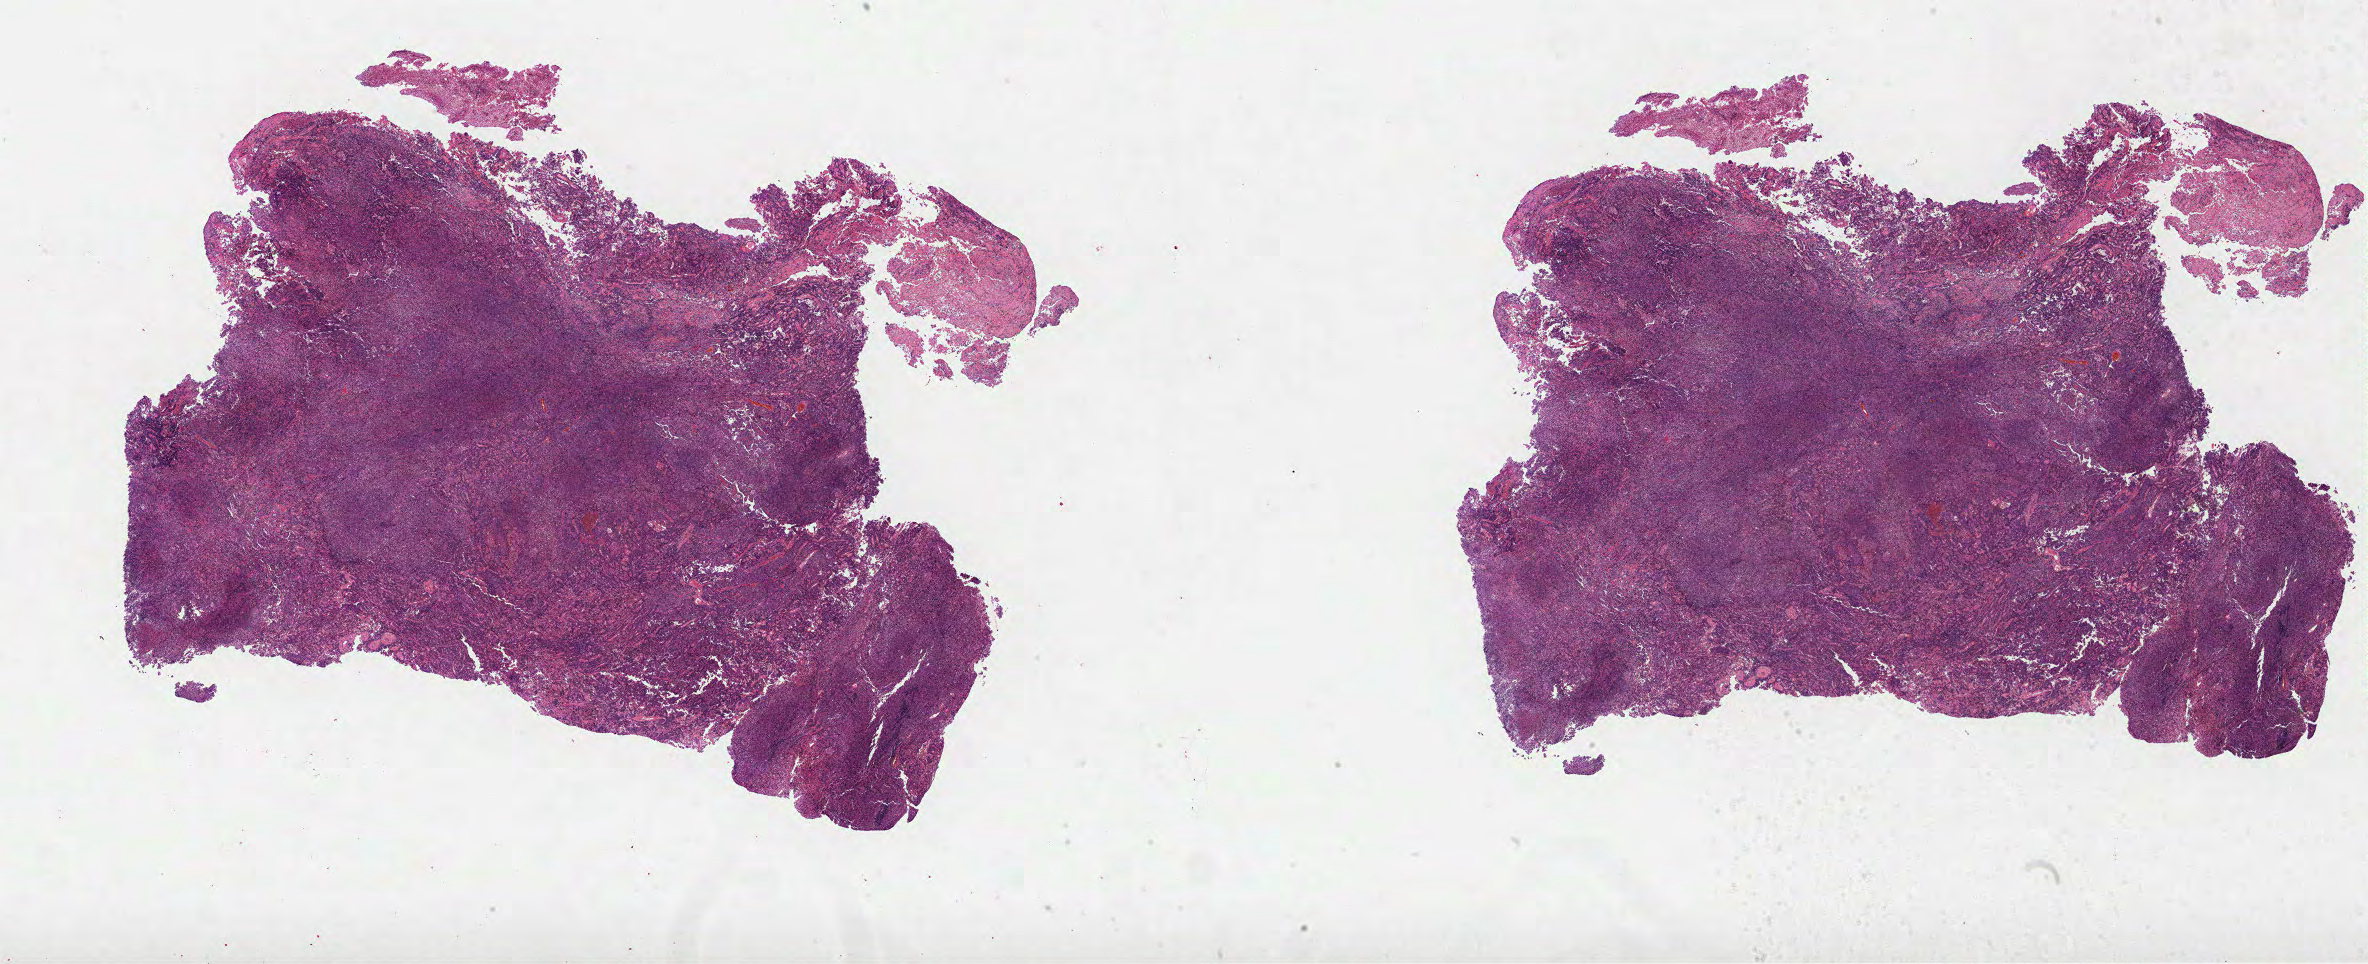
H&E whole-slide image, a low-resolution overview of the entire scanned area, about 38.2 x 15.5 mm (acquisition: 40x scan); formalin-fixed paraffin-embedded (FFPE) diagnostic section; lung, primary tumour sample. Male patient; age at initial diagnosis 69 years.
Pathologic diagnosis: Squamous cell carcinoma, NOS (upper lobe, lung). AJCC pathologic stage: IB (7th edition). TNM: T2 N0 M0.